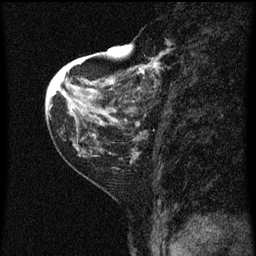
Breast MRI (dynamic contrast-enhanced), one sagittal slice. Position 20 of 60 along the scan axis. Dynamic contrast-enhanced series, image 2 of 3 at this slice position (ordered by acquisition). 1.5 T. TE 4.2 ms, TR 8 ms. 2 mm slice thickness. 256 × 256 image matrix, field of view 180 × 180 mm. Patient: female, 48 years.
Structures marked on this image (semi-automatic segmentation, software-assisted and operator-edited):
- analysis volume of interest (the breast-tissue region the enhancement analysis was run in; not a lesion): box from (x=128, y=54) to (x=175, y=125) px
- tumour enhancement mask (voxels above the 70 % enhancement threshold inside the analysis volume of interest): (x=132, y=54)–(x=165, y=125)